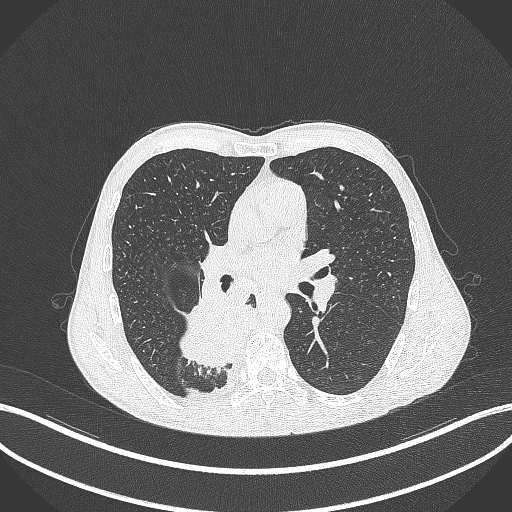
Chest CT, one axial slice; position 205 of 371 along the scan axis; reconstruction kernel B70f; 120 kVp; lung window (W 1500 / L -600 HU); 512 × 512 image matrix, field of view 400 × 400 mm. Male patient, age 58 years. From the clinical record (not read from this slice): clinical TNM (as recorded): T3 N1 M1.
Structures marked on this image (rectangle marked by the reading radiologist):
- lung tumour (recorded histology: squamous cell carcinoma): bounding box [x1, y1, x2, y2] px = [172, 290, 252, 372]